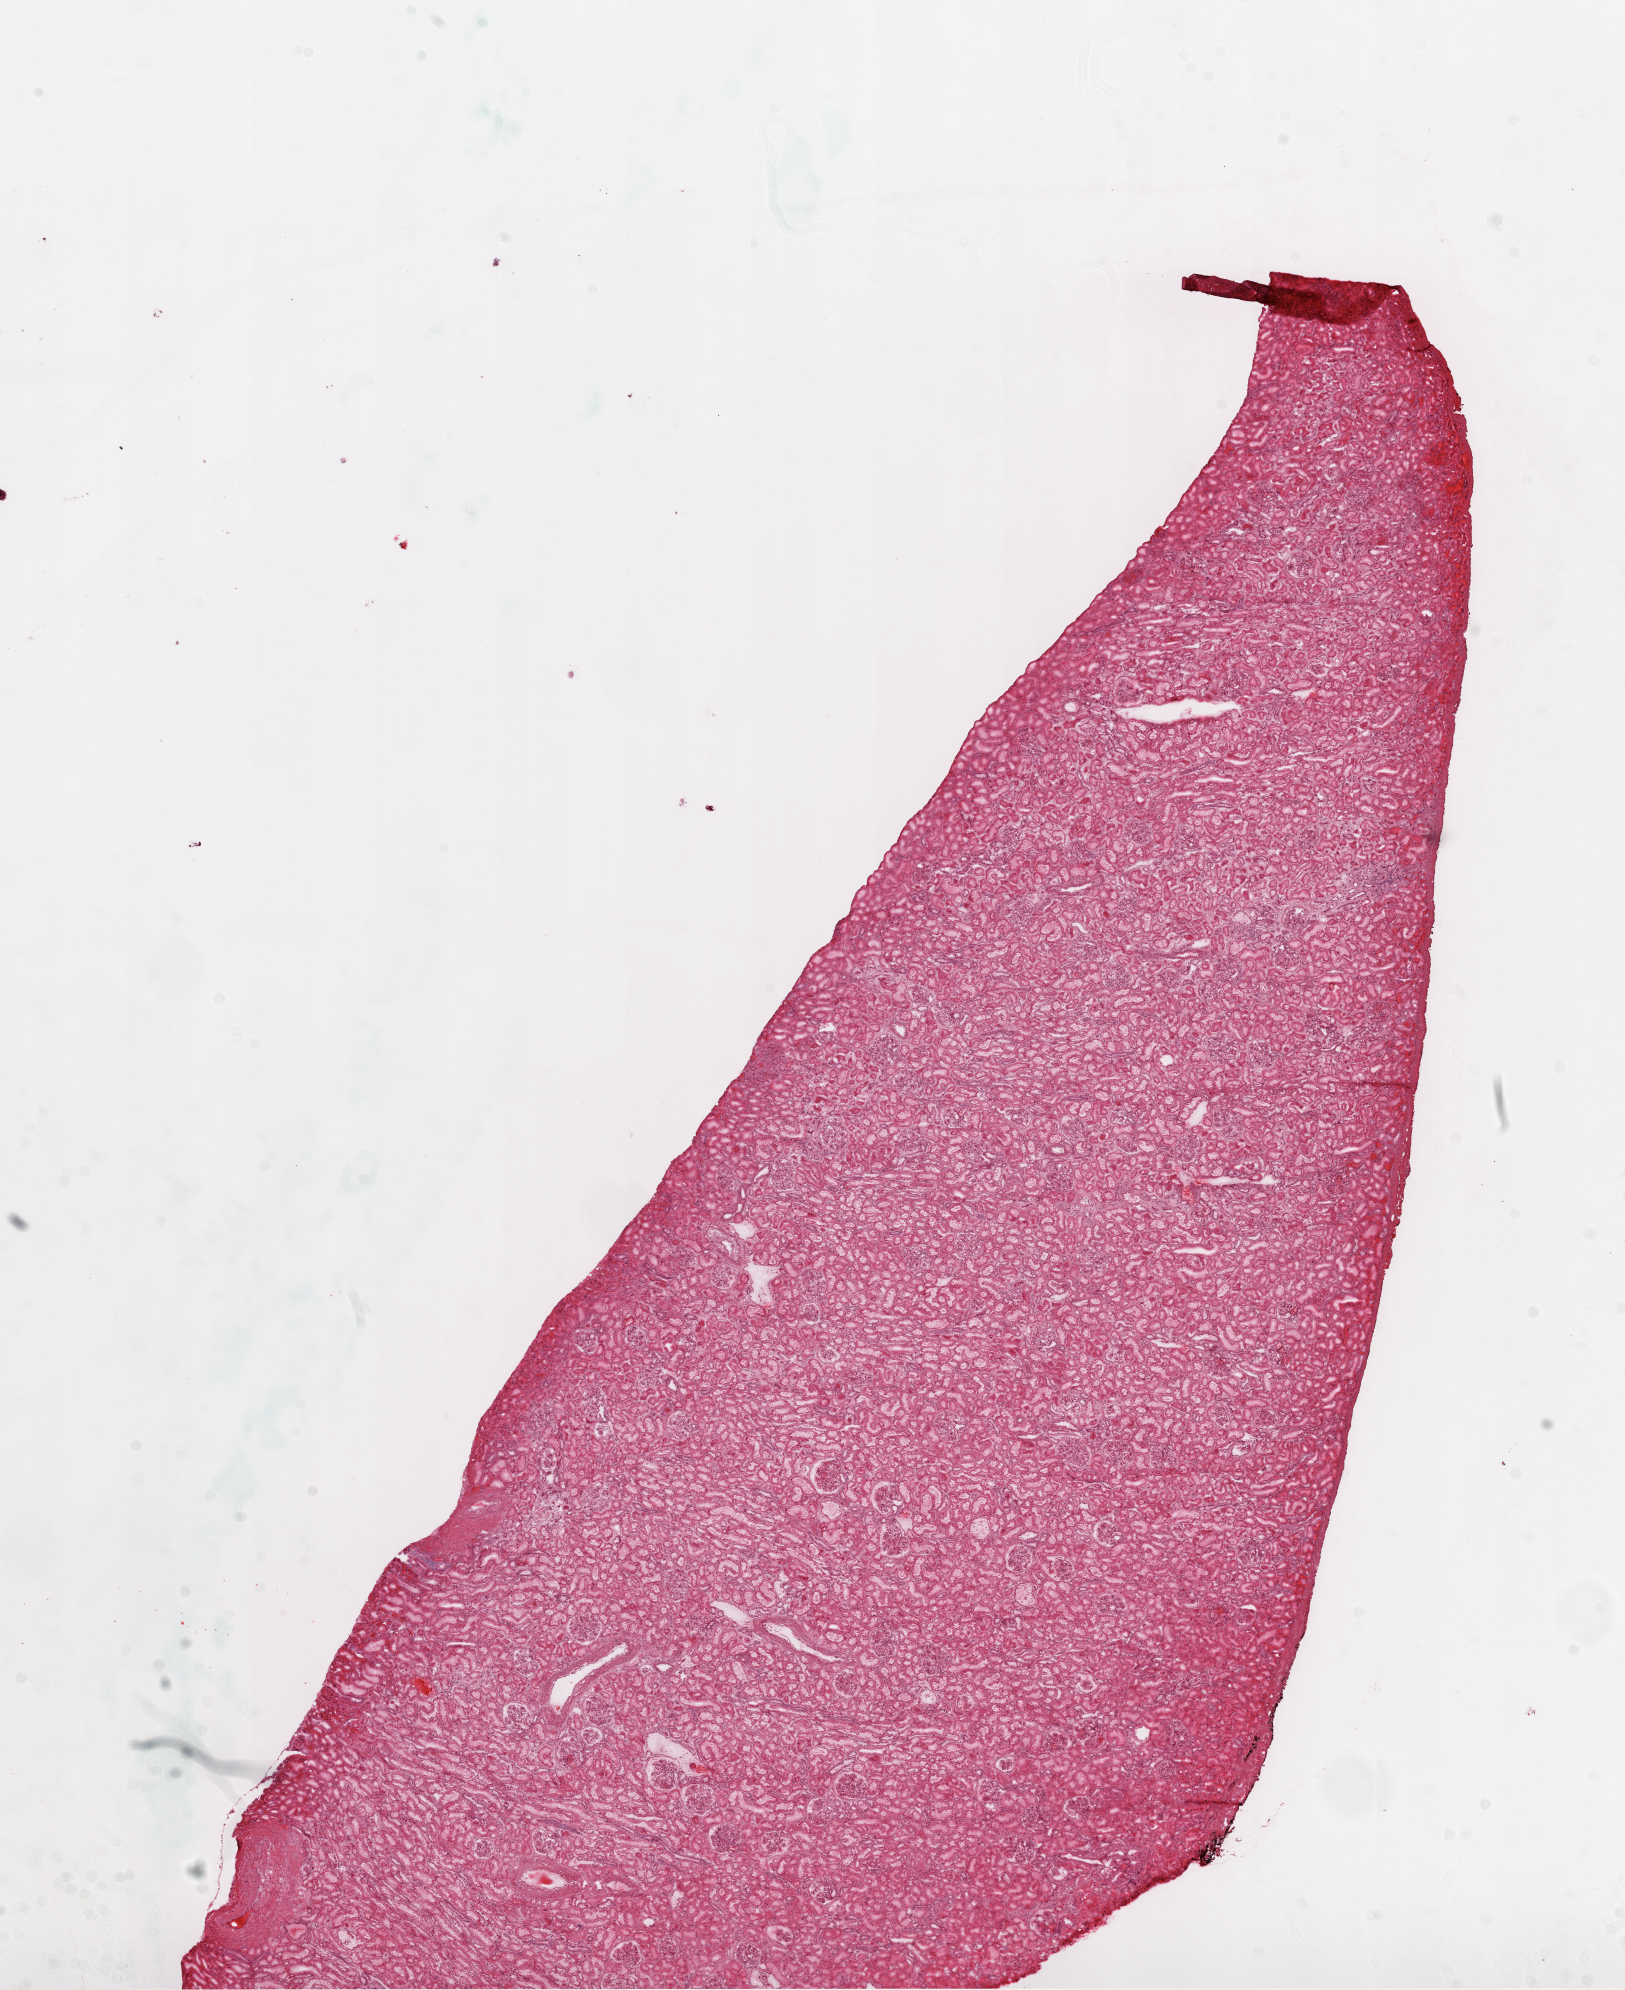
H&E-stained whole-slide image, shown as a low-resolution overview of the whole scanned area (about 13.0 x 16.0 mm). Frozen section from the top of the tissue portion. Solid tissue normal (non-tumour tissue) sample from the kidney. Male, age 62 years at initial diagnosis.
This section: solid tissue normal (non-tumour) sample from the same patient. Patient diagnosis: Clear cell adenocarcinoma, NOS.